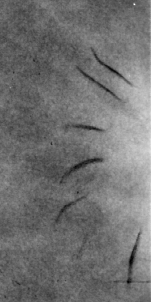
Cropped region of a digitized screen-film mammogram centred on a radiologist-marked abnormality, right breast, CC view, BI-RADS breast density category 2 (scale 1–4).
Finding: mass, shape architectural distortion, margins spiculated; BI-RADS assessment category 4; subtlety rating 2 on a 1 (subtle) to 5 (obvious) scale; pathology result (as recorded, not read from the image): malignant.